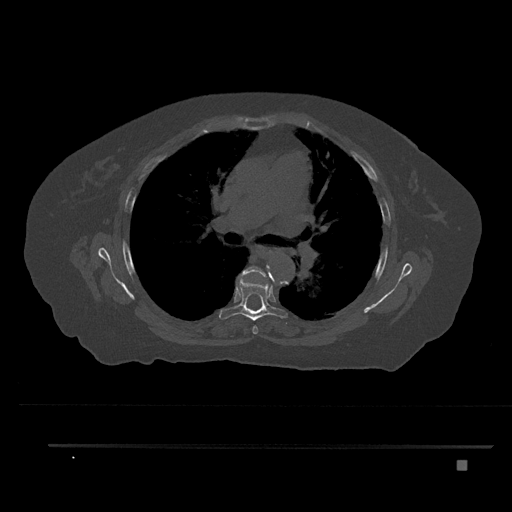
CT including the spine, one axial slice. Position 536 of 797 along the scan axis. 120 kVp. Bone window (W 1800 / L 400 HU). 512 × 512 image matrix. Patient: female, 76 years. From the clinical record (not read from this slice): primary cancer: lung; vertebrae with lytic lesions (as recorded): T11, L3.
Outlined on this slice (semi-automatic segmentation, software-assisted and operator-edited):
- T5 vertebra: box from (x=237, y=266) to (x=268, y=334) px
- T6 vertebra: (x=219, y=275)–(x=288, y=321)